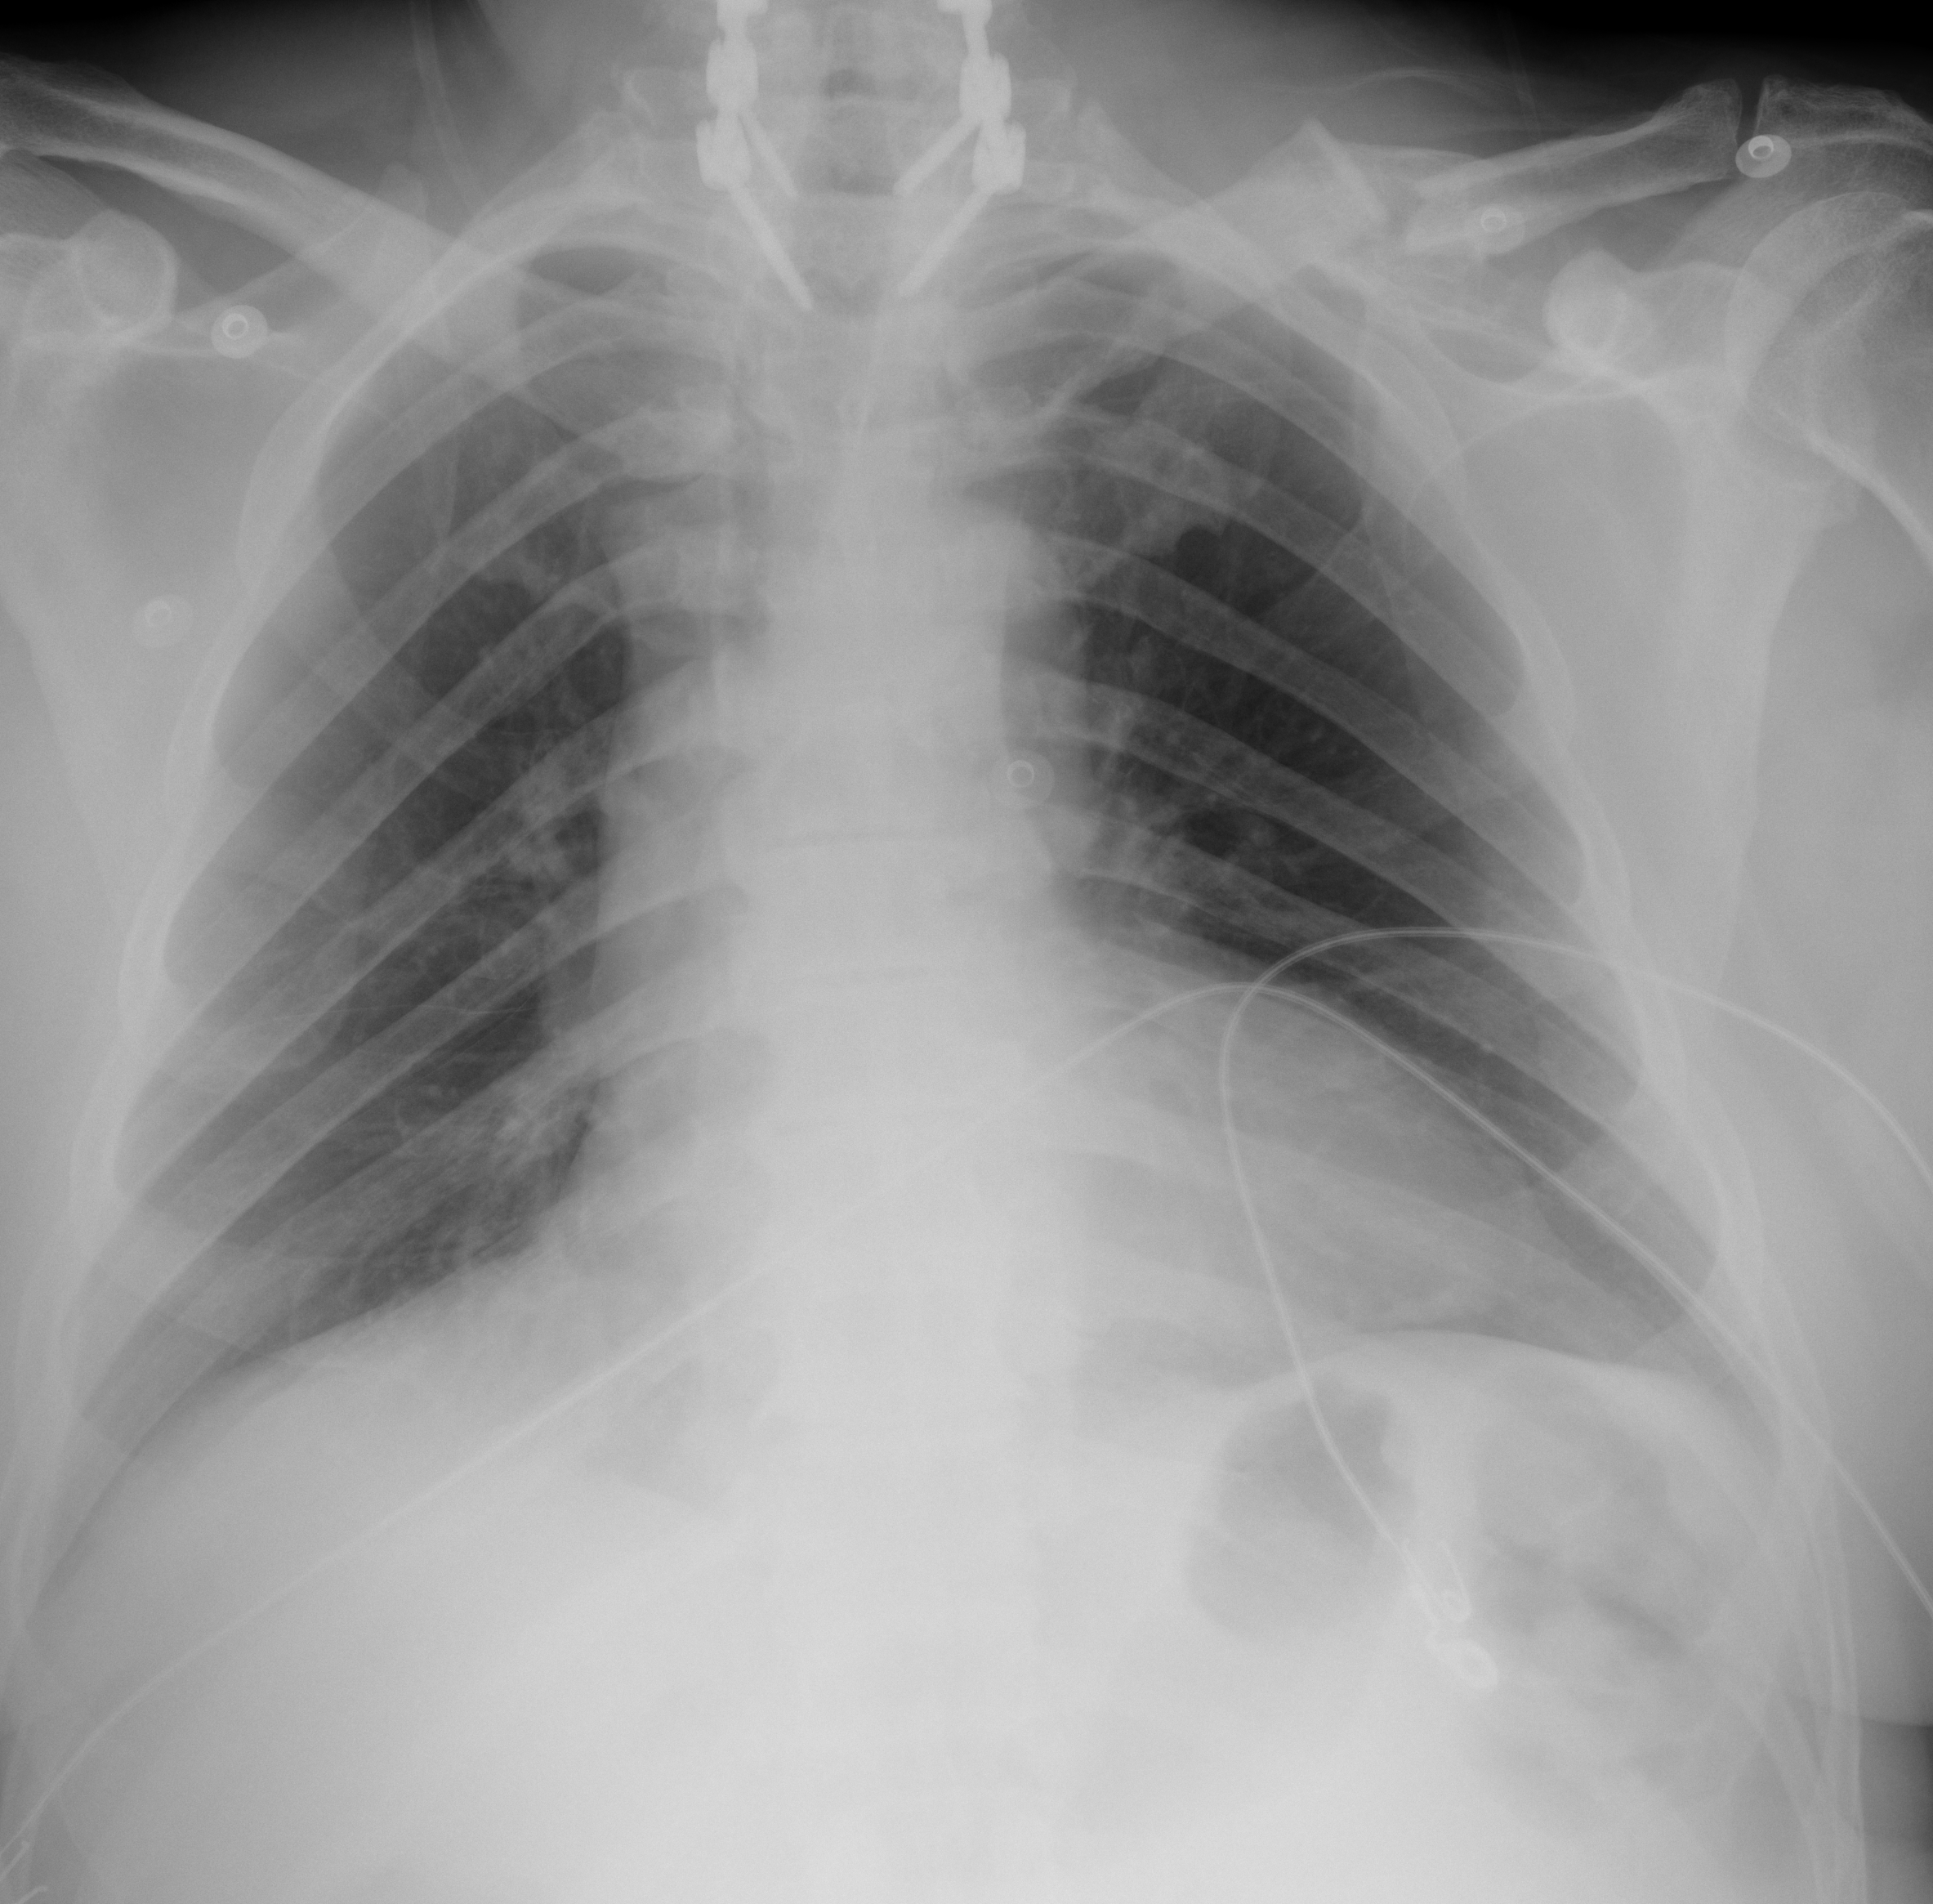
Portable chest radiograph, AP projection. Male patient, age 77 years; imaged 0 days after the COVID-19 diagnosis.
Key findings recorded by the radiologist: No focal consolidation in the lungs.